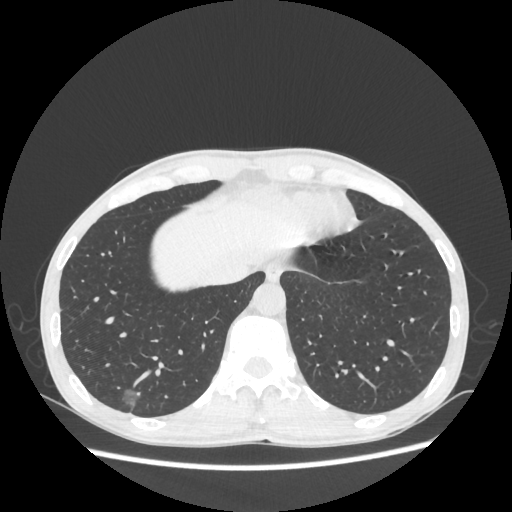
Chest CT, one axial slice. Slice 63 of 270 in the series (ordered by position). Reconstruction kernel STANDARD. 100 kVp. Lung window (W 1500 / L -600 HU). 1.25 mm slice thickness. 512 × 512 image matrix, field of view 360 × 360 mm. Male patient, age 60 years. From the clinical record (not read from this slice): clinical TNM (as recorded): T1c N0 M0; histopathological grade: G2.
Annotated regions visible in this slice (bounding box drawn by a radiologist):
- lung tumour (recorded histology: adenocarcinoma): bounding box [x1, y1, x2, y2] px = [116, 377, 140, 411]